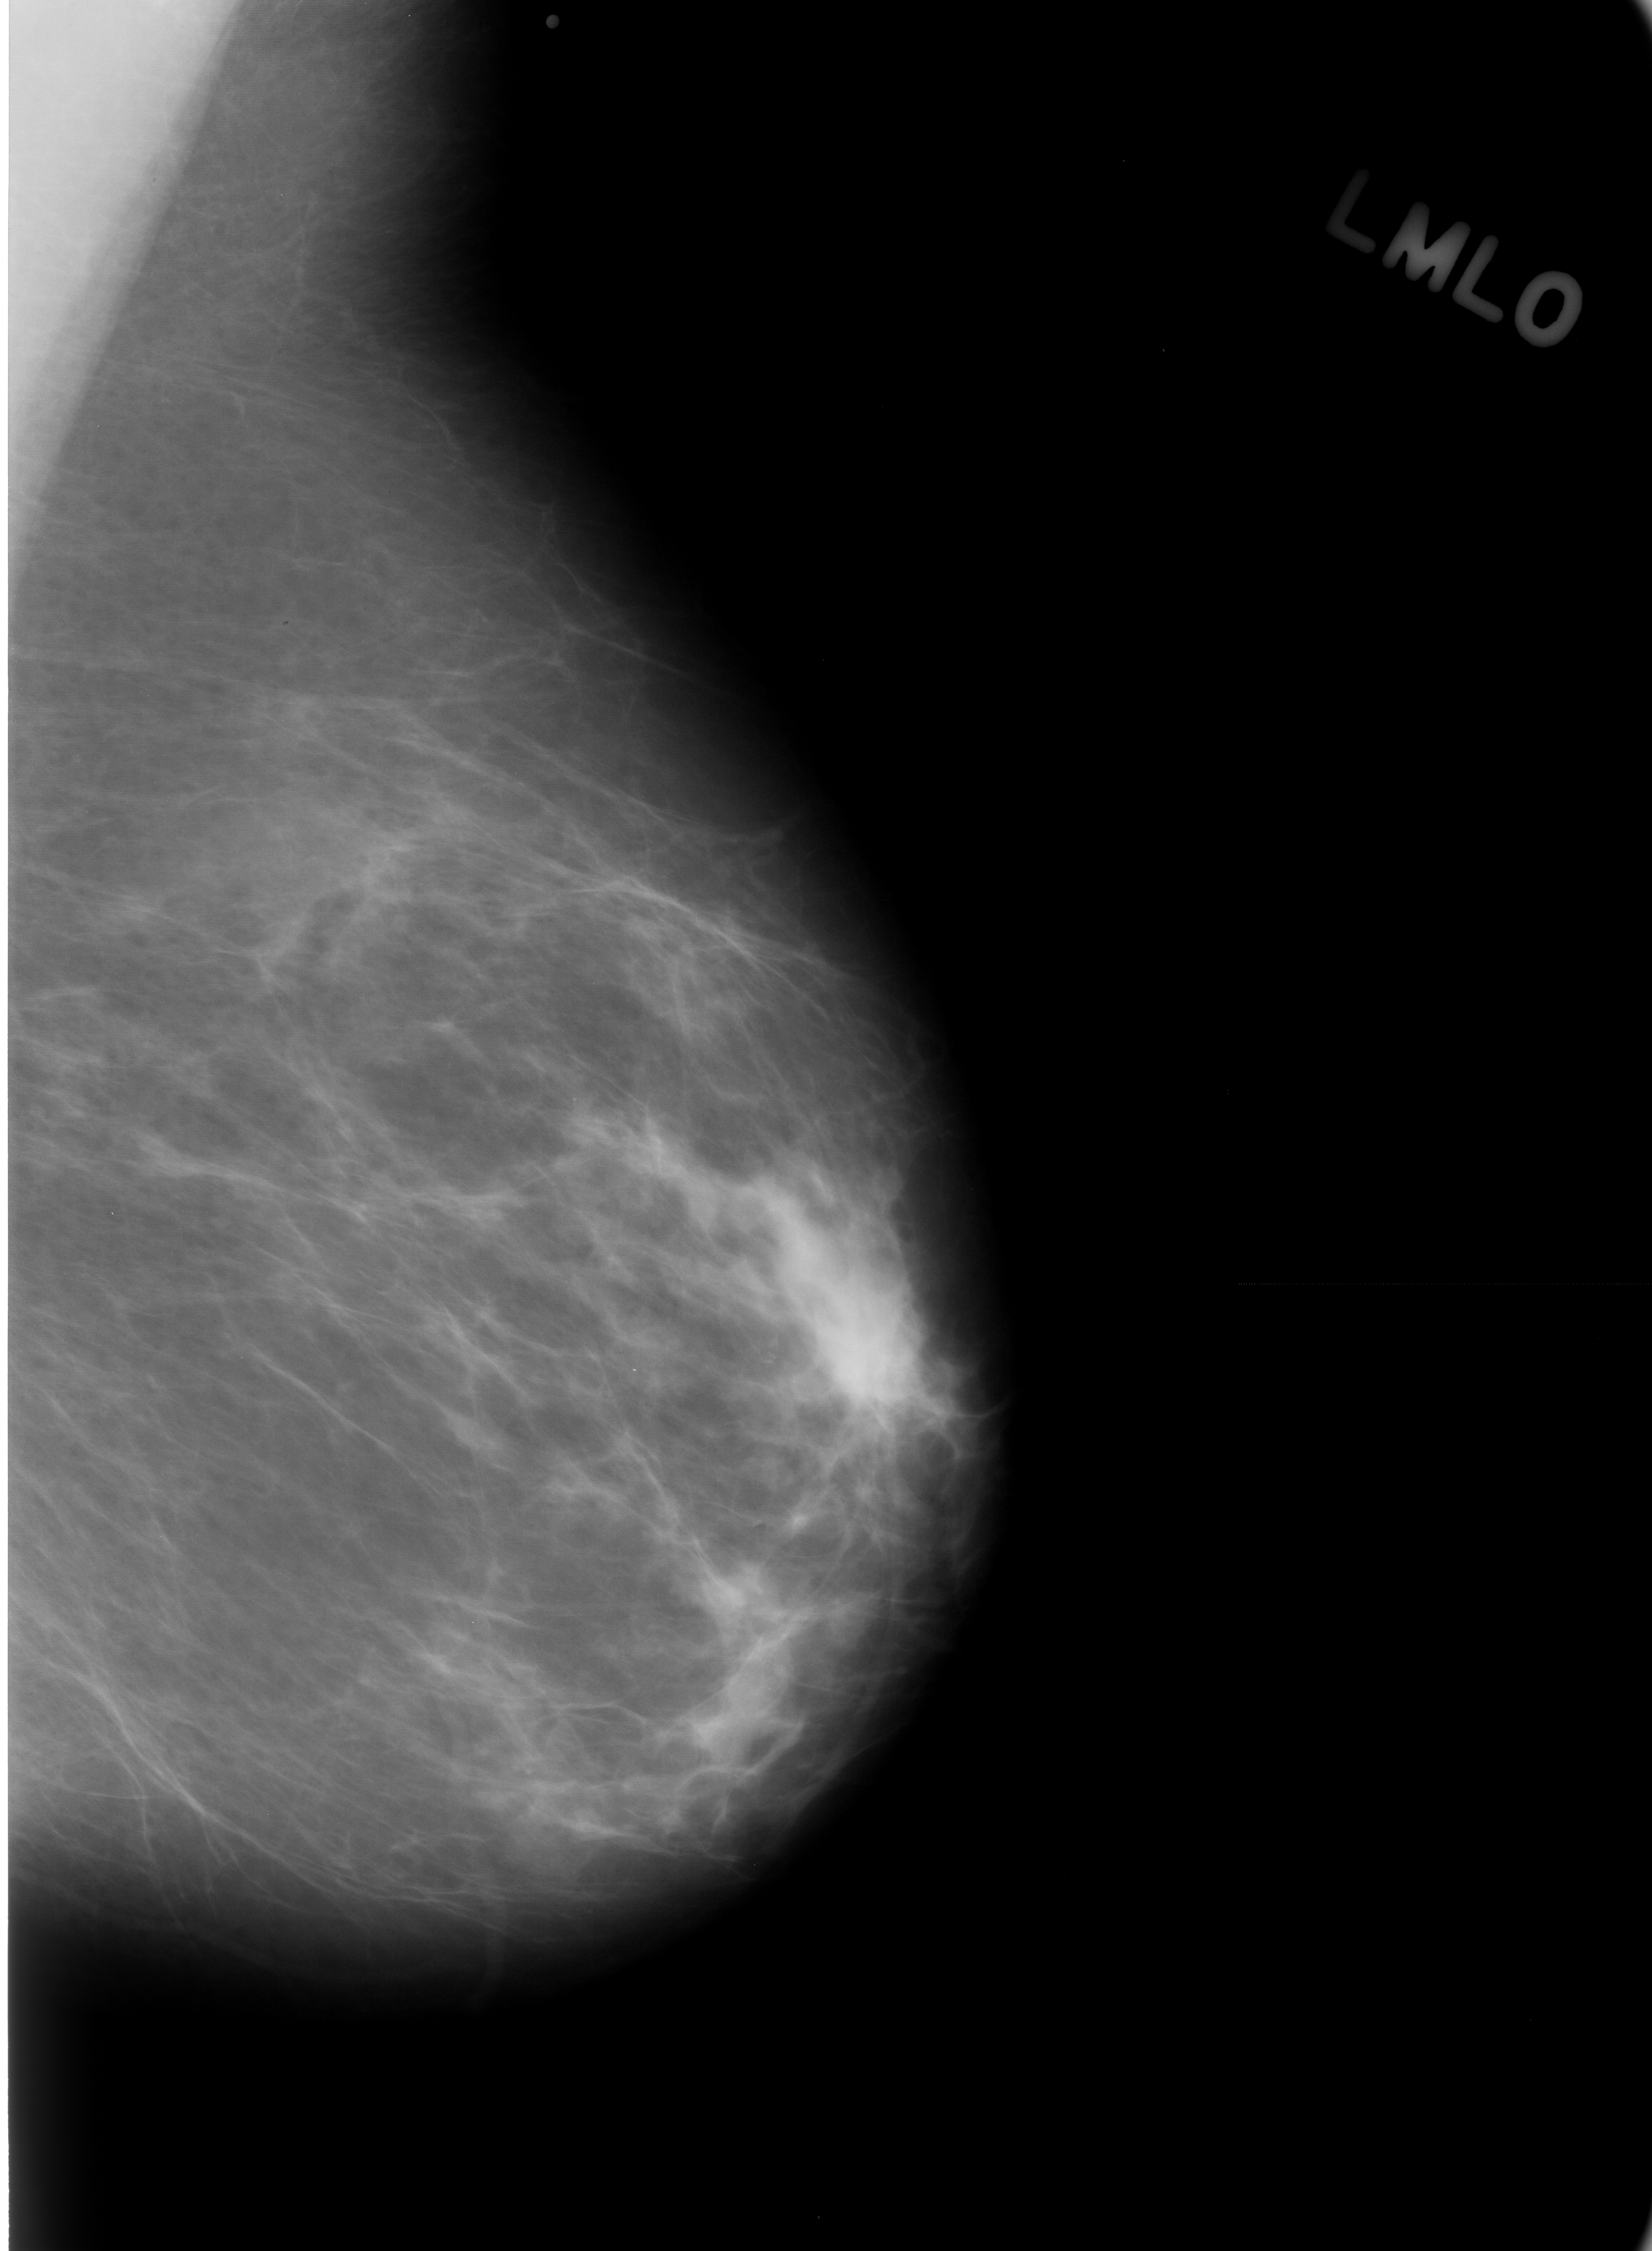
Mammogram (digitized film); left breast; MLO view; breast composition: scattered fibroglandular densities (BI-RADS density category 2 of 4); 1652 × 2251 image matrix.
Marked abnormalities (boxes around the expert regions of interest):
- calcifications, morphology pleomorphic, distribution clustered; BI-RADS assessment category 4; pathology (as recorded): benign: bounding box (x1, y1, x2, y2) in pixels: (133, 888, 275, 1029)